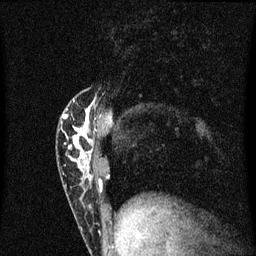
Breast MRI (dynamic contrast-enhanced), one sagittal slice; slice 17 of 60 in the series (ordered by position); dynamic contrast-enhanced series, image 2 of 3 at this slice position (ordered by acquisition); 1.5 T; TE 4.2 ms, TR 8.4 ms; 256 × 256 image matrix, field of view 200 × 200 mm. Female patient, age 40 years.
Annotated regions visible in this slice (semi-automatically segmented with operator editing):
- analysis volume of interest (the breast-tissue region the enhancement analysis was run in; not a lesion): bounding box [x1, y1, x2, y2] px = [59, 98, 103, 203]
- tumour enhancement mask (voxels above the 70 % enhancement threshold inside the analysis volume of interest): [63, 100, 101, 181]